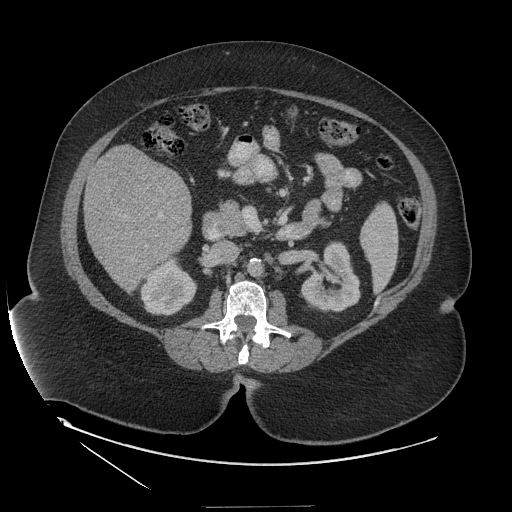
Contrast-enhanced abdominal CT (liver protocol), one axial slice. Slice 51 of 127 in the series (ordered by position). Reconstruction kernel STANDARD. Soft-tissue window (W 400 / L 40 HU). 2.5 mm slice thickness. 512 × 512 image matrix. From the clinical record (not read from this slice): diagnosis: hepatocellular carcinoma (patient treated with transarterial chemoembolisation; whether this scan precedes or follows treatment is not stated here); TNM stage (as recorded): Stage-II; Child-Pugh class: A; tumour differentiation: well differentiated.
Structures marked on this image (semi-automatic segmentation, software-assisted and operator-edited):
- liver parenchyma outside the tumour (the mass and vessels are separate outlines, so this box may not span the whole liver): bounding box <84,144,192,290> (left, top, right, bottom; pixels)